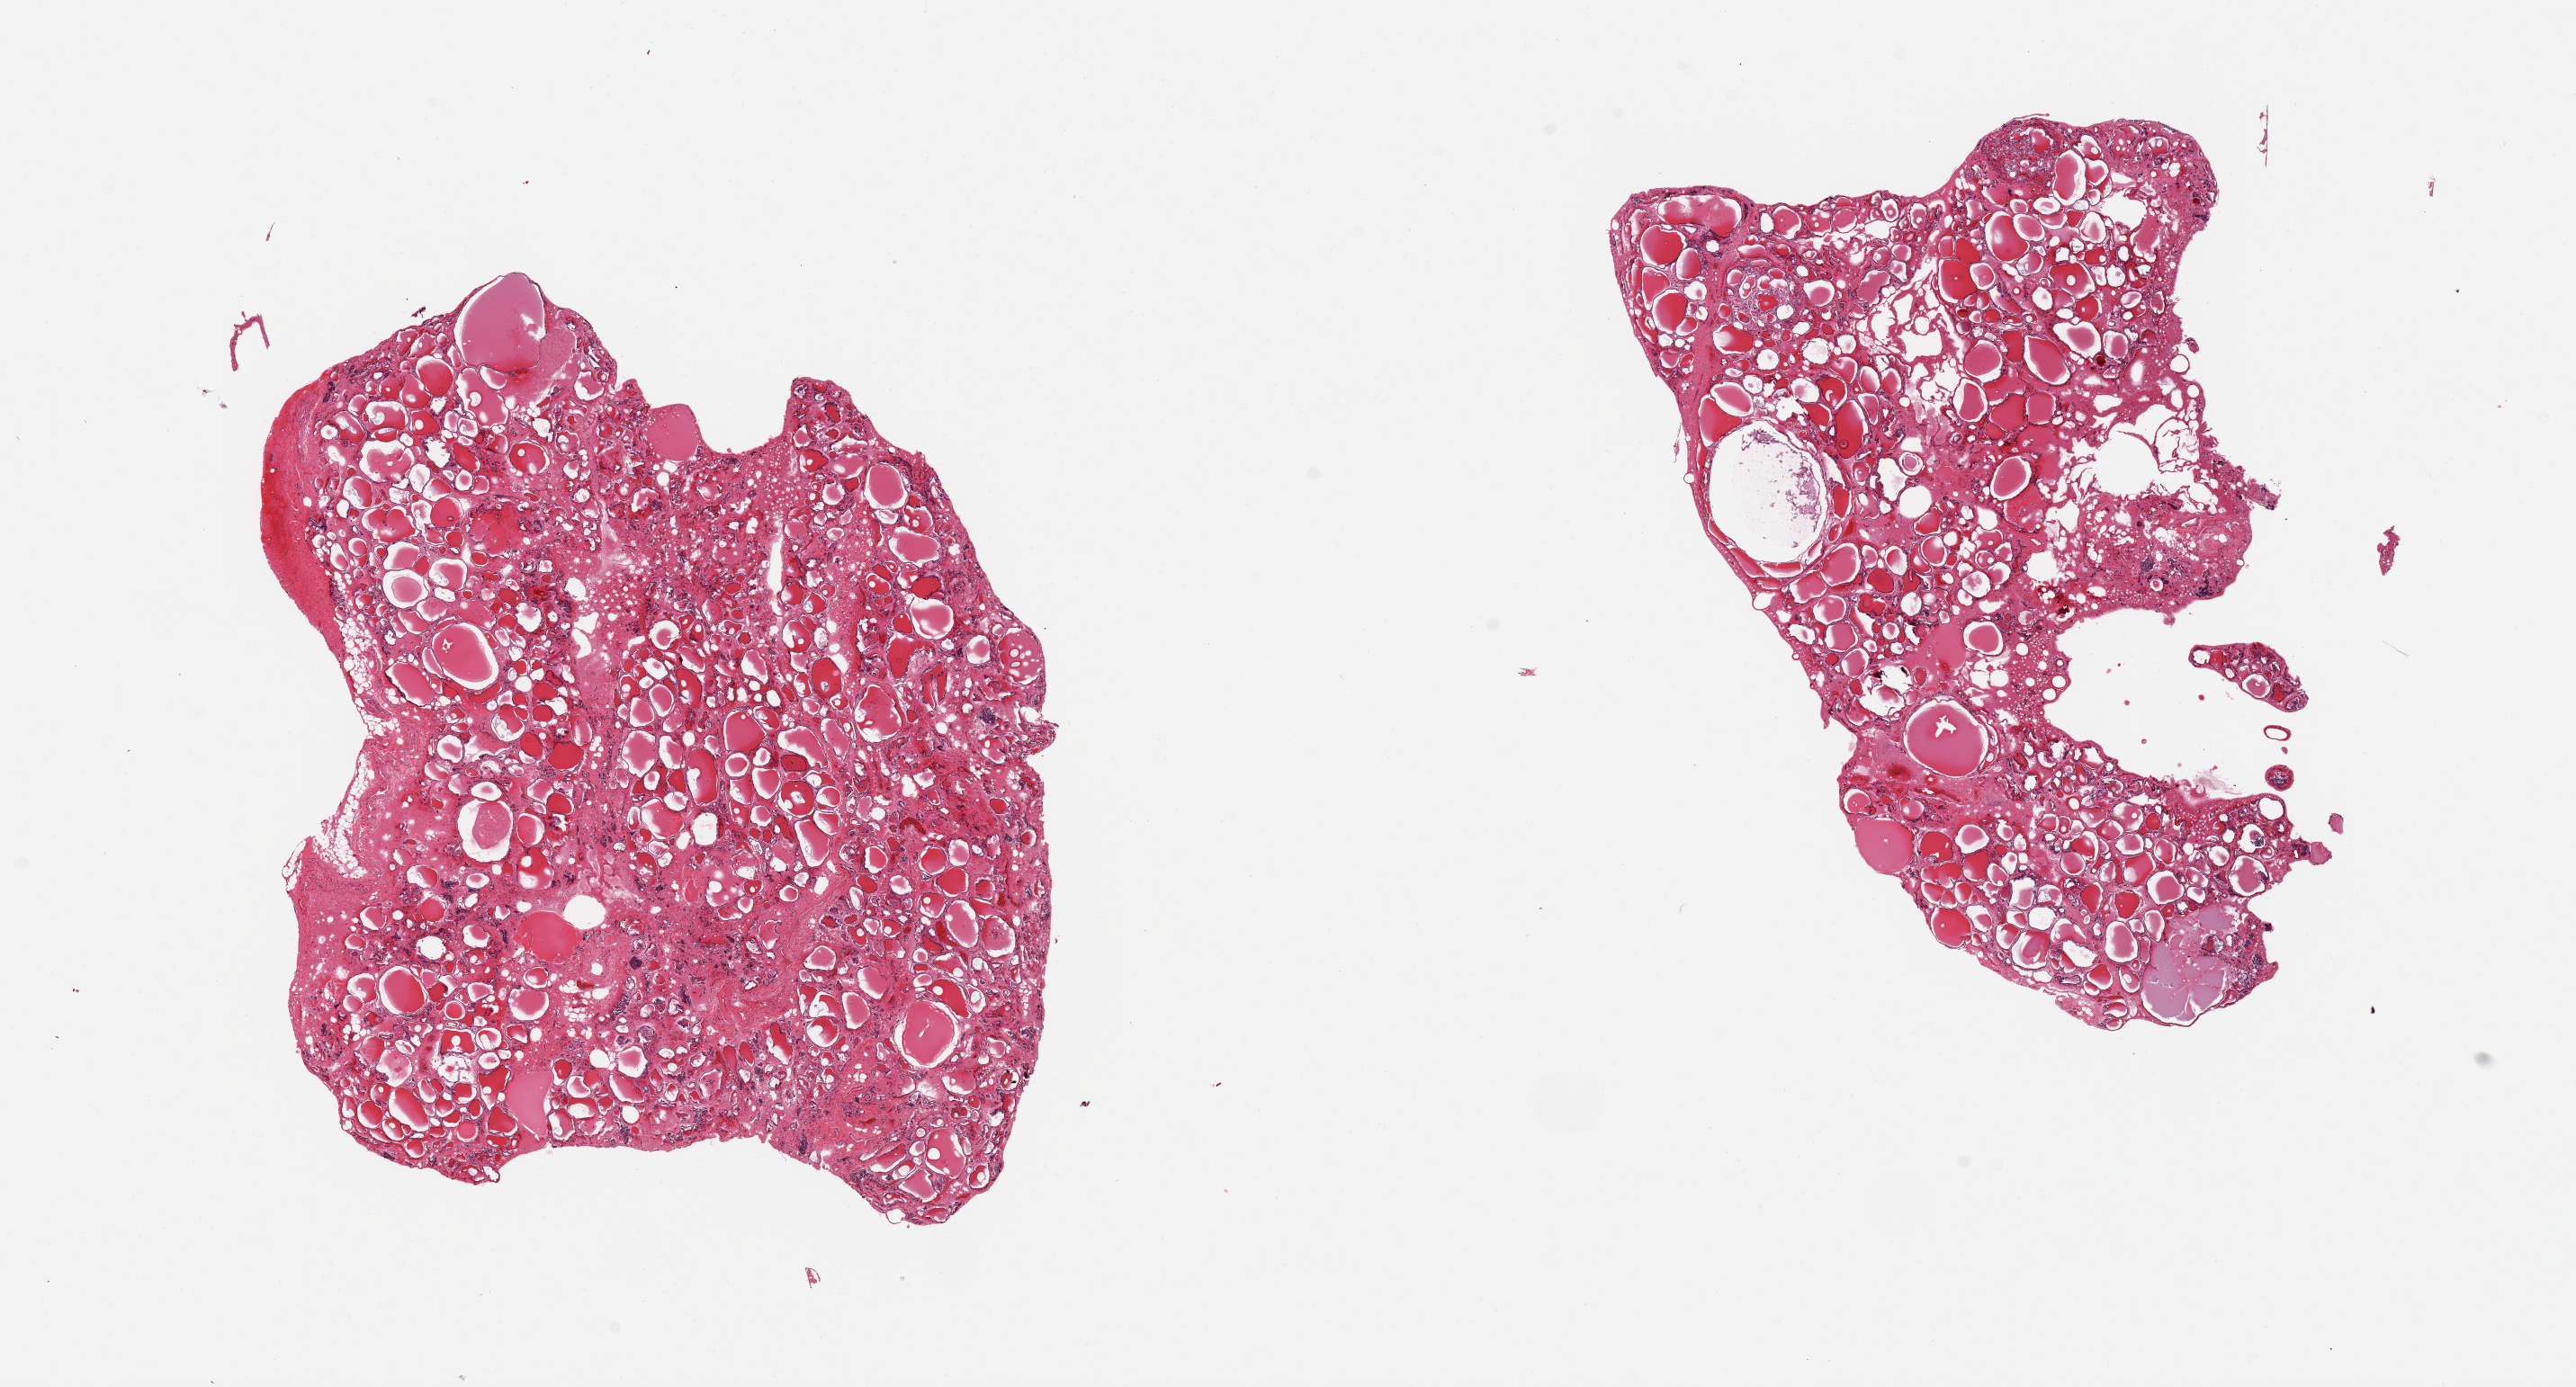
H&E whole-slide image — shown as a low-resolution overview of the whole scanned area (about 22.6 x 12.2 mm, acquisition: 20x scan). PAXgene-fixed, paraffin-embedded tissue. Section of thyroid (target tissue). Donor tissue sample. Donor: male.
• pathologist's review note for this sample: 2 pieces; features of multinodular goiter